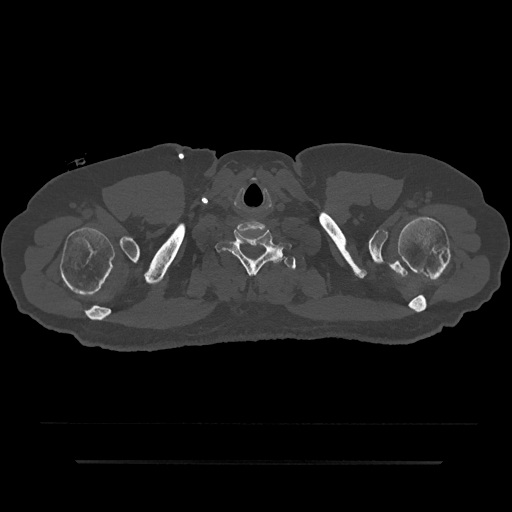
CT including the spine, one axial slice; position 771 of 797 along the scan axis; 120 kVp; bone window (W 1800 / L 400 HU); 512 × 512 image matrix, field of view 464 × 464 mm. Male patient, age 59 years. From the clinical record (not read from this slice): primary cancer: bile ducts; vertebrae with lytic lesions (as recorded): T10.
Structures marked on this image (semi-automatically segmented with operator editing):
- T1 vertebra: bounding box (x1, y1, x2, y2) in pixels: (273, 255, 296, 270)